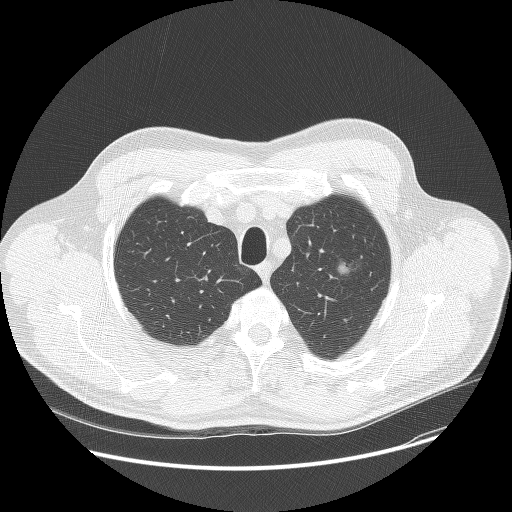
Chest CT (low-dose screening protocol), one axial image. Baseline screening round. Lung window (W 1500 / L -600 HU). 2.5 mm slice thickness. Slice 21 of 132 in the series. 512 × 512 image matrix, field of view 400 × 400 mm. Male participant, aged 60 years at enrolment.
Expert-annotated lung lesion, bounding box (x1, y1, x2, y2) in pixels: (320, 247, 371, 290). The screening reader recorded 2 non-calcified nodules or masses ≥4 mm on this exam (left upper lobe, right lower lobe); which of them this box marks is not recorded. Participant outcome: lung cancer diagnosed 784 days after this screen (after the third annual screen) — bronchiolo-alveolar carcinoma, non-mucinous, left upper lobe, well differentiated (G1), stage IA (AJCC 6th edition), 16 mm at pathology.